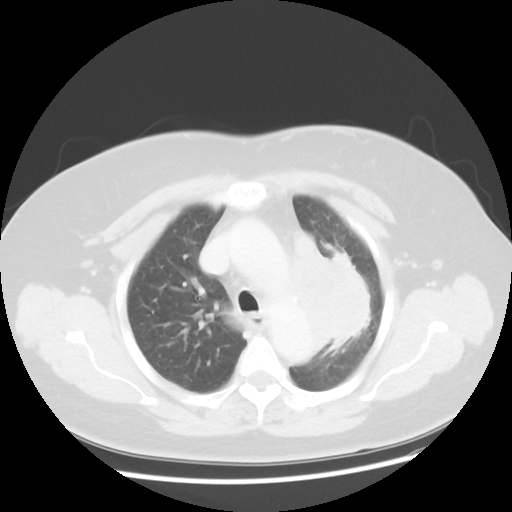
Chest CT, one axial slice. Position 35 of 49 along the scan axis. 120 kVp. Lung window (W 1500 / L -600 HU). 5 mm slice thickness. 512 × 512 image matrix, field of view 374 × 374 mm. Patient: female, 58 years. From the clinical record (not read from this slice): clinical TNM (as recorded): T4 N3 M0.
Outlined on this slice (bounding box drawn by a radiologist):
- lung tumour (recorded histology: small cell carcinoma): box from (x=289, y=235) to (x=380, y=349) px